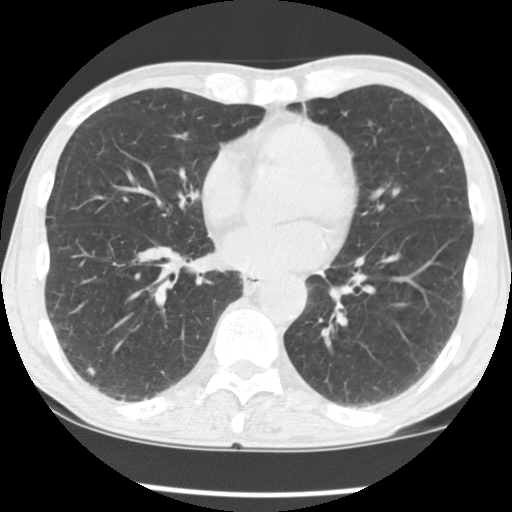
Axial slice from a low-dose chest CT screening exam, baseline screening round, lung window (W 1500 / L -600 HU), 2.5 mm slice thickness, slice 79 of 135 in the series. Male participant, aged 68 years at enrolment. Current smoker at enrolment.
Expert-annotated lung lesion, bounding box (x1, y1, x2, y2) in pixels: (72, 356, 111, 393). The screening reader recorded 4 non-calcified nodules or masses ≥4 mm on this exam (right middle lobe, left upper lobe, right lower lobe, right lower lobe); which of them this box marks is not recorded. Official screen result: positive, change unspecified: nodule(s) >= 4 mm or enlarging nodule(s), mass(es), or other non-specific abnormalities suspicious for lung cancer. Lung cancer was diagnosed 284 days after this screen: adenocarcinoma, NOS, right lower lobe, moderately differentiated (G2), stage IV (AJCC 6th edition), 14 mm at pathology.